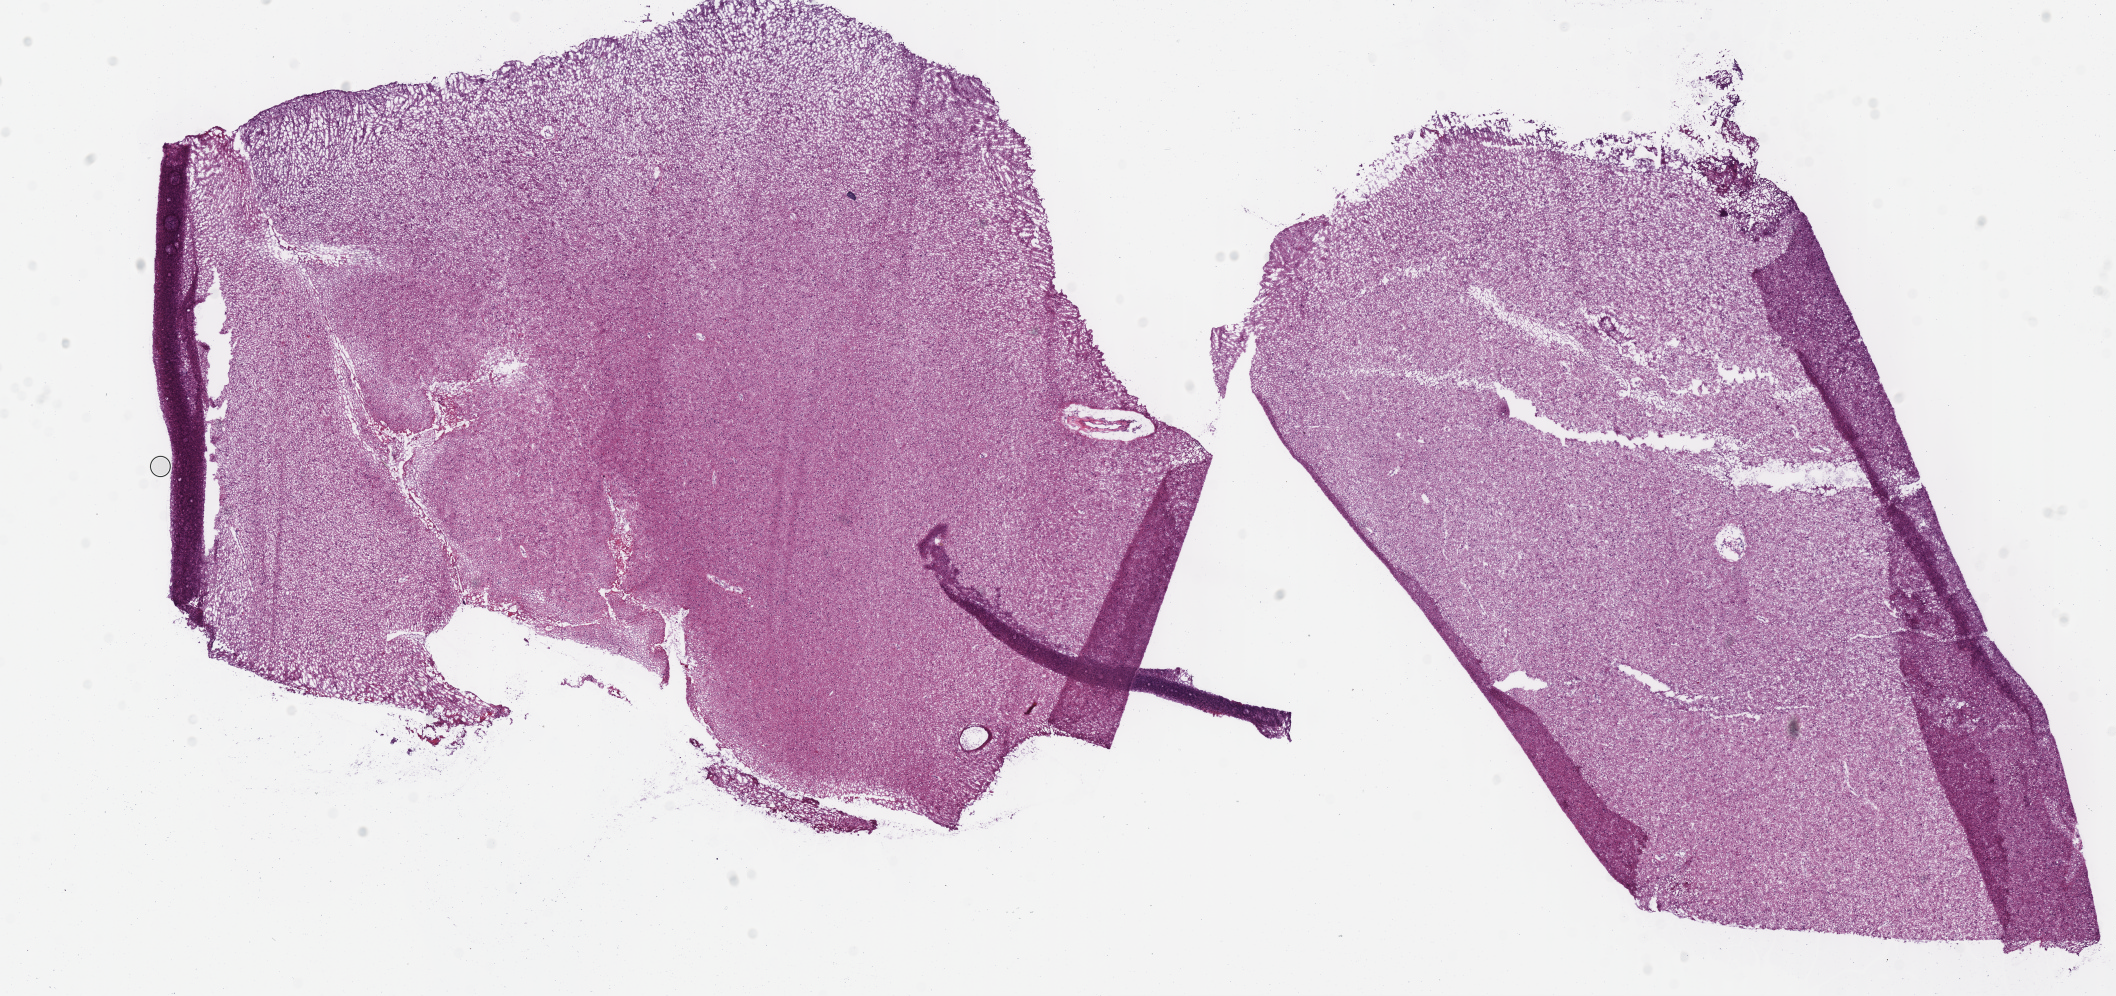
Hematoxylin and eosin (H&E) stained whole-slide image, a low-resolution overview of the entire scanned area, about 16.6 x 7.8 mm (acquisition: 40x scan), frozen section, primary tumour sample from the brain. Male, age 32 years at initial diagnosis. Histologic grade: G3 (poorly differentiated). Slide review estimates, as recorded: tumour cells 100%, tumour nuclei 70%, normal cells 0%, stromal cells 0%, necrosis 0%.
• histologic diagnosis: Mixed glioma (cerebrum)
• laterality: left